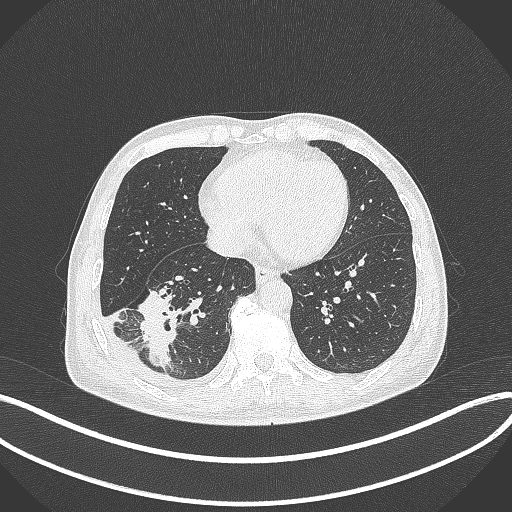
Chest CT, one axial slice; position 128 of 388 along the scan axis; 120 kVp; lung window (W 1500 / L -600 HU); 512 × 512 image matrix, field of view 400 × 400 mm. Patient: male, 64 years. Case-level facts recorded for this patient, not image findings: clinical TNM (as recorded): T3 N0 M0; histopathological grade: G2-3.
Outlined on this slice (rectangle marked by the reading radiologist):
- lung tumour (recorded histology: adenocarcinoma): box from (x=132, y=283) to (x=182, y=371) px